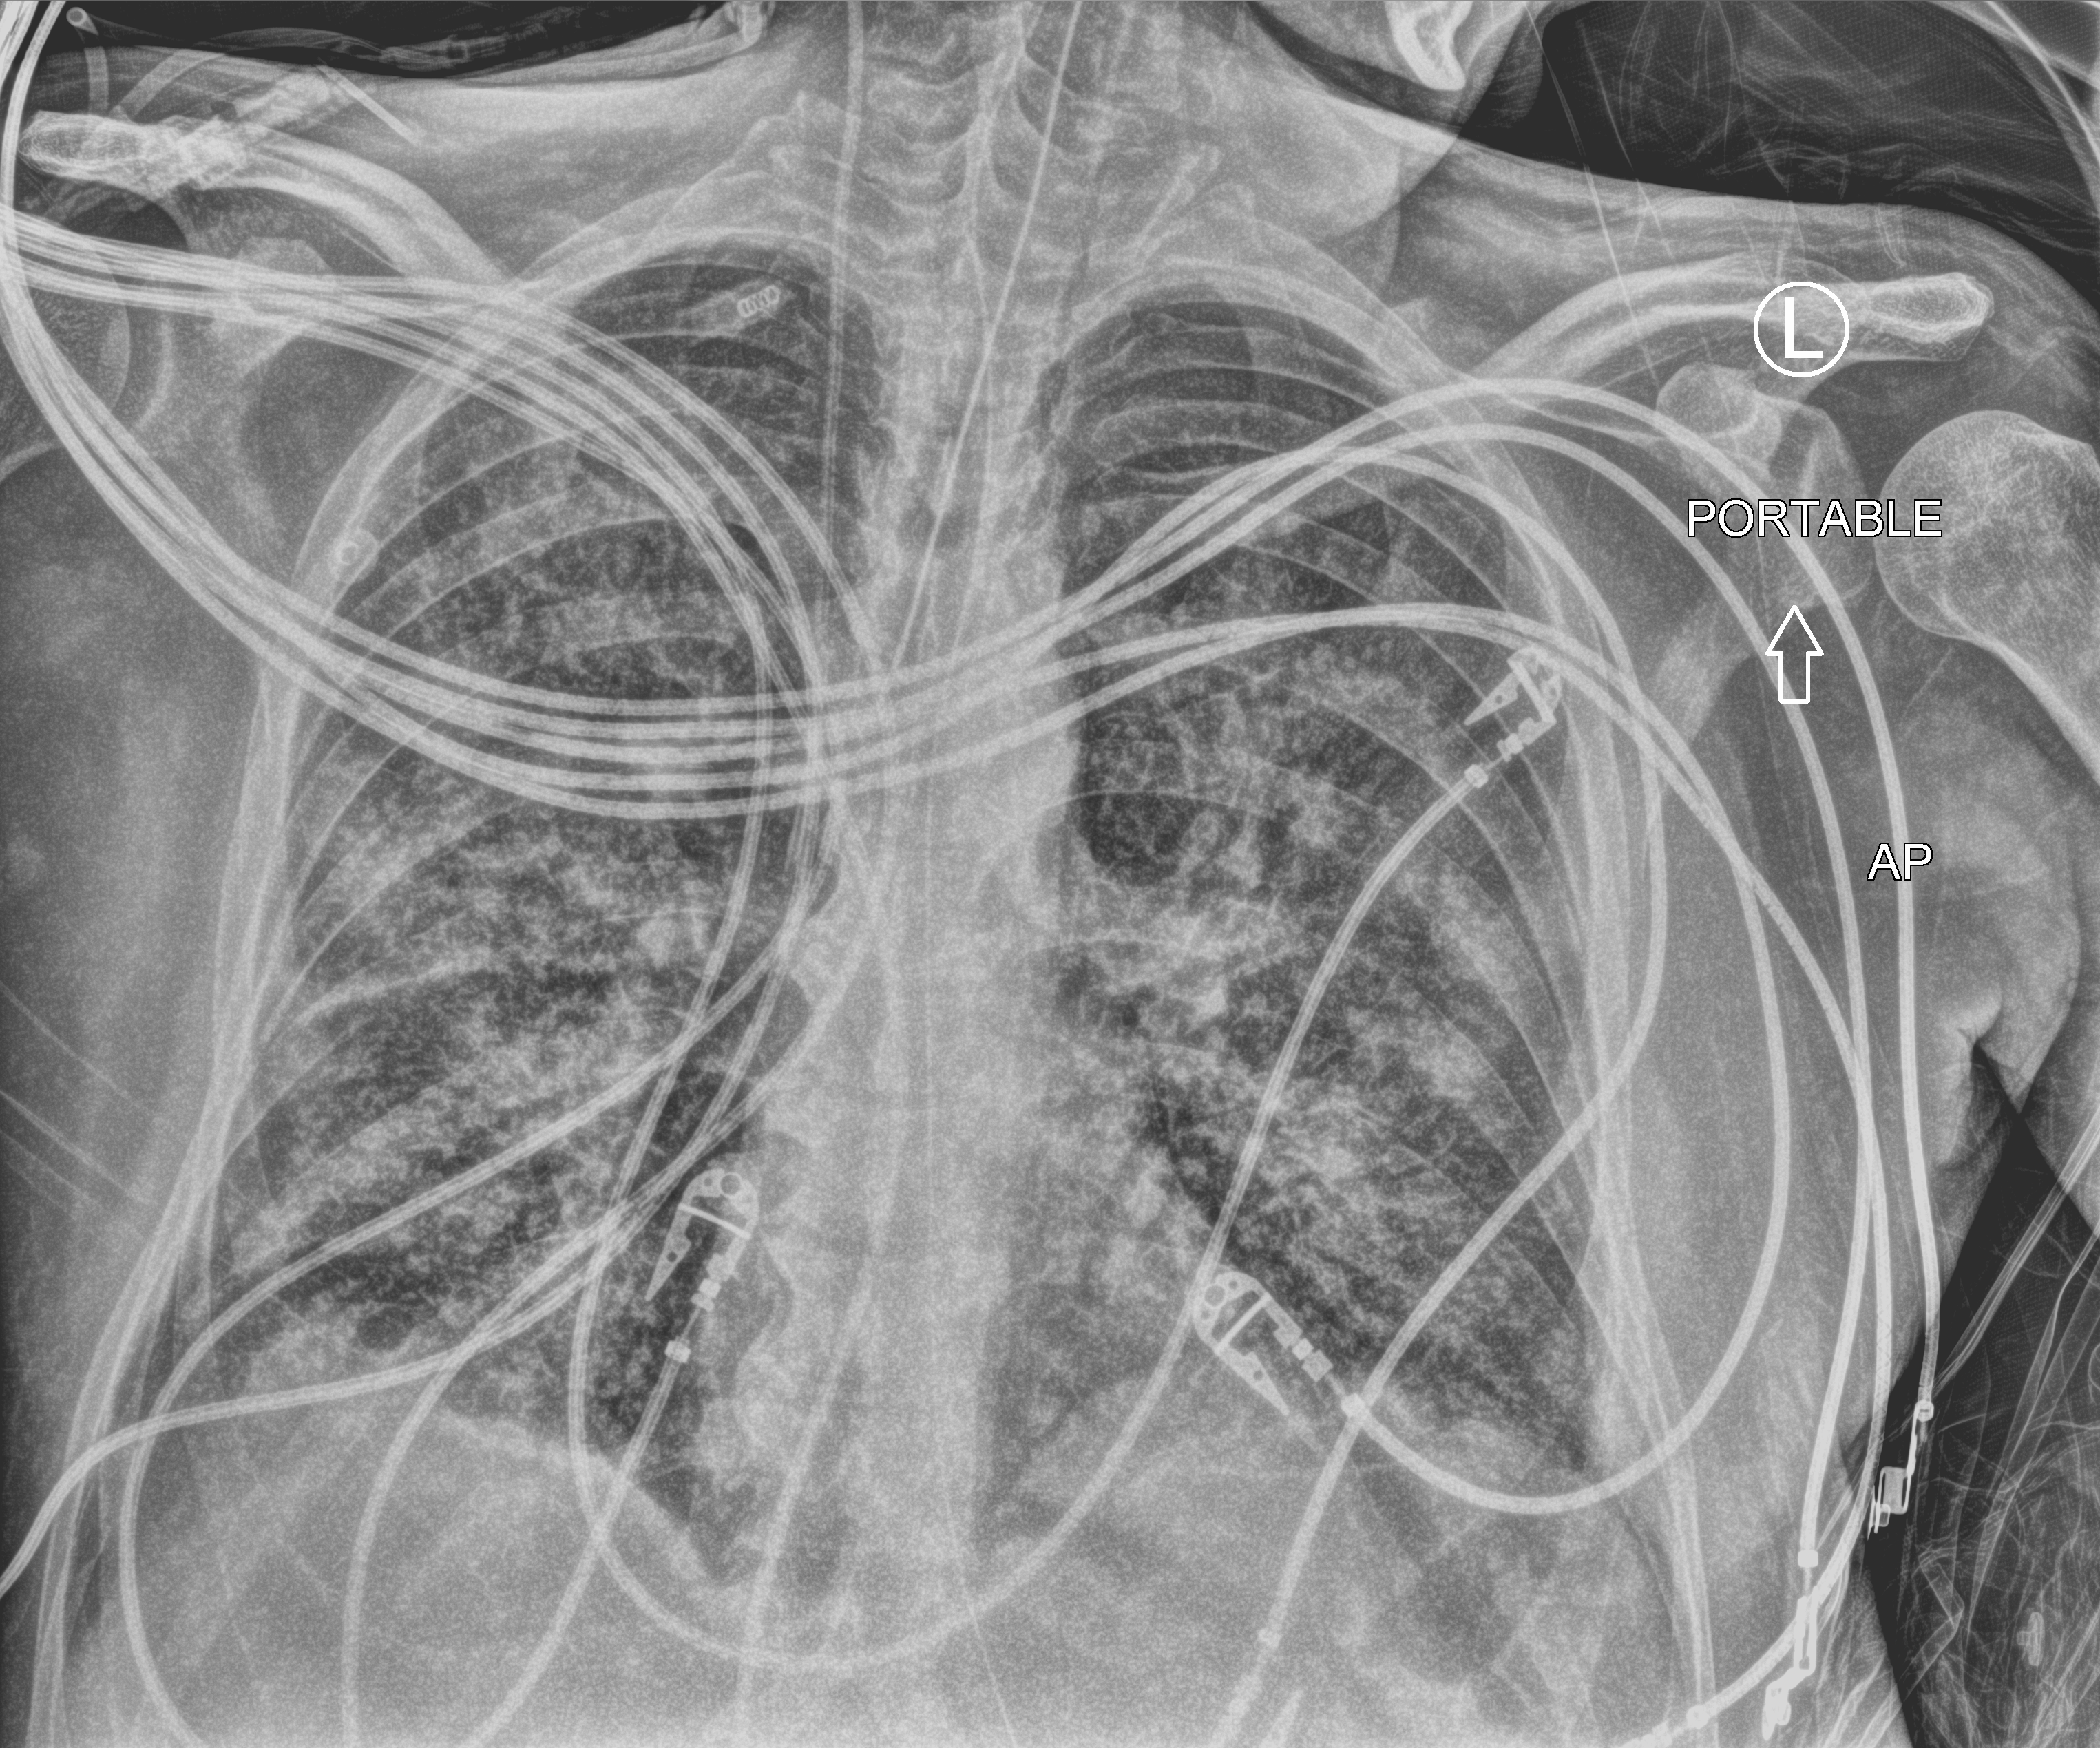
Portable chest radiograph, anteroposterior (AP) projection. Male patient hospitalised with COVID-19, age 60–74 years.
Hospital-stay facts (about this admission, not read from this image; timing relative to this image not recorded): diabetes (admission record): yes; admitted to intensive care during this hospital stay: yes; mechanically ventilated during this hospital stay: yes.